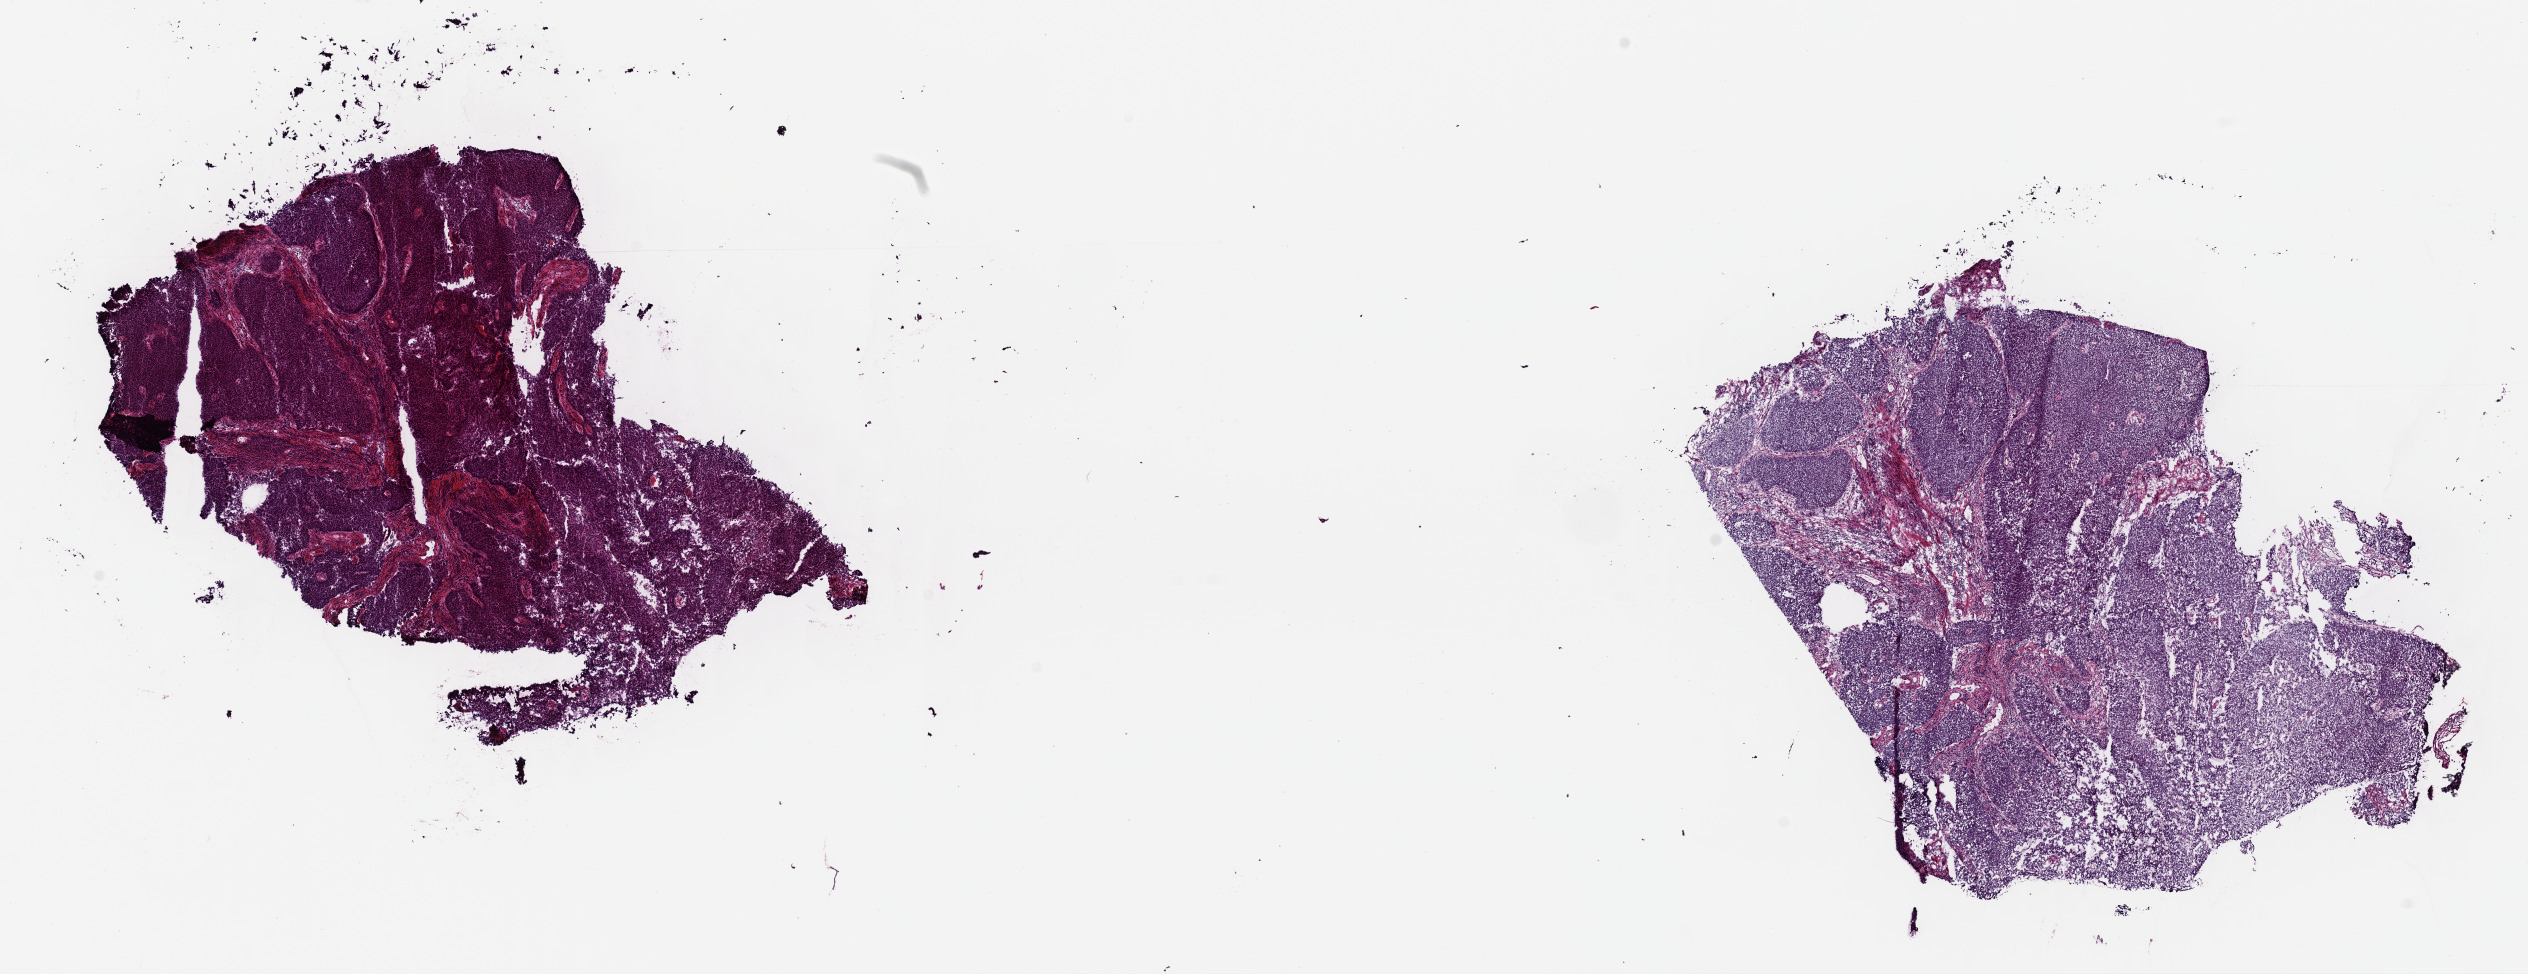
H&E-stained whole-slide image — a low-resolution overview of the entire scanned area, about 20.0 x 7.7 mm (slide scanned at 40x); frozen section from the top of the tissue portion; primary tumour sample from the bladder. Patient: male, age at initial diagnosis 69 years. Slide review estimates, as recorded: tumour cells 100%, tumour nuclei 95%, normal cells 0%, stromal cells 0%, necrosis 0%. Inflammatory infiltration, as recorded: lymphocyte infiltration 0%, monocyte infiltration 0%, neutrophil infiltration 0%.
* histologic diagnosis: Transitional cell carcinoma